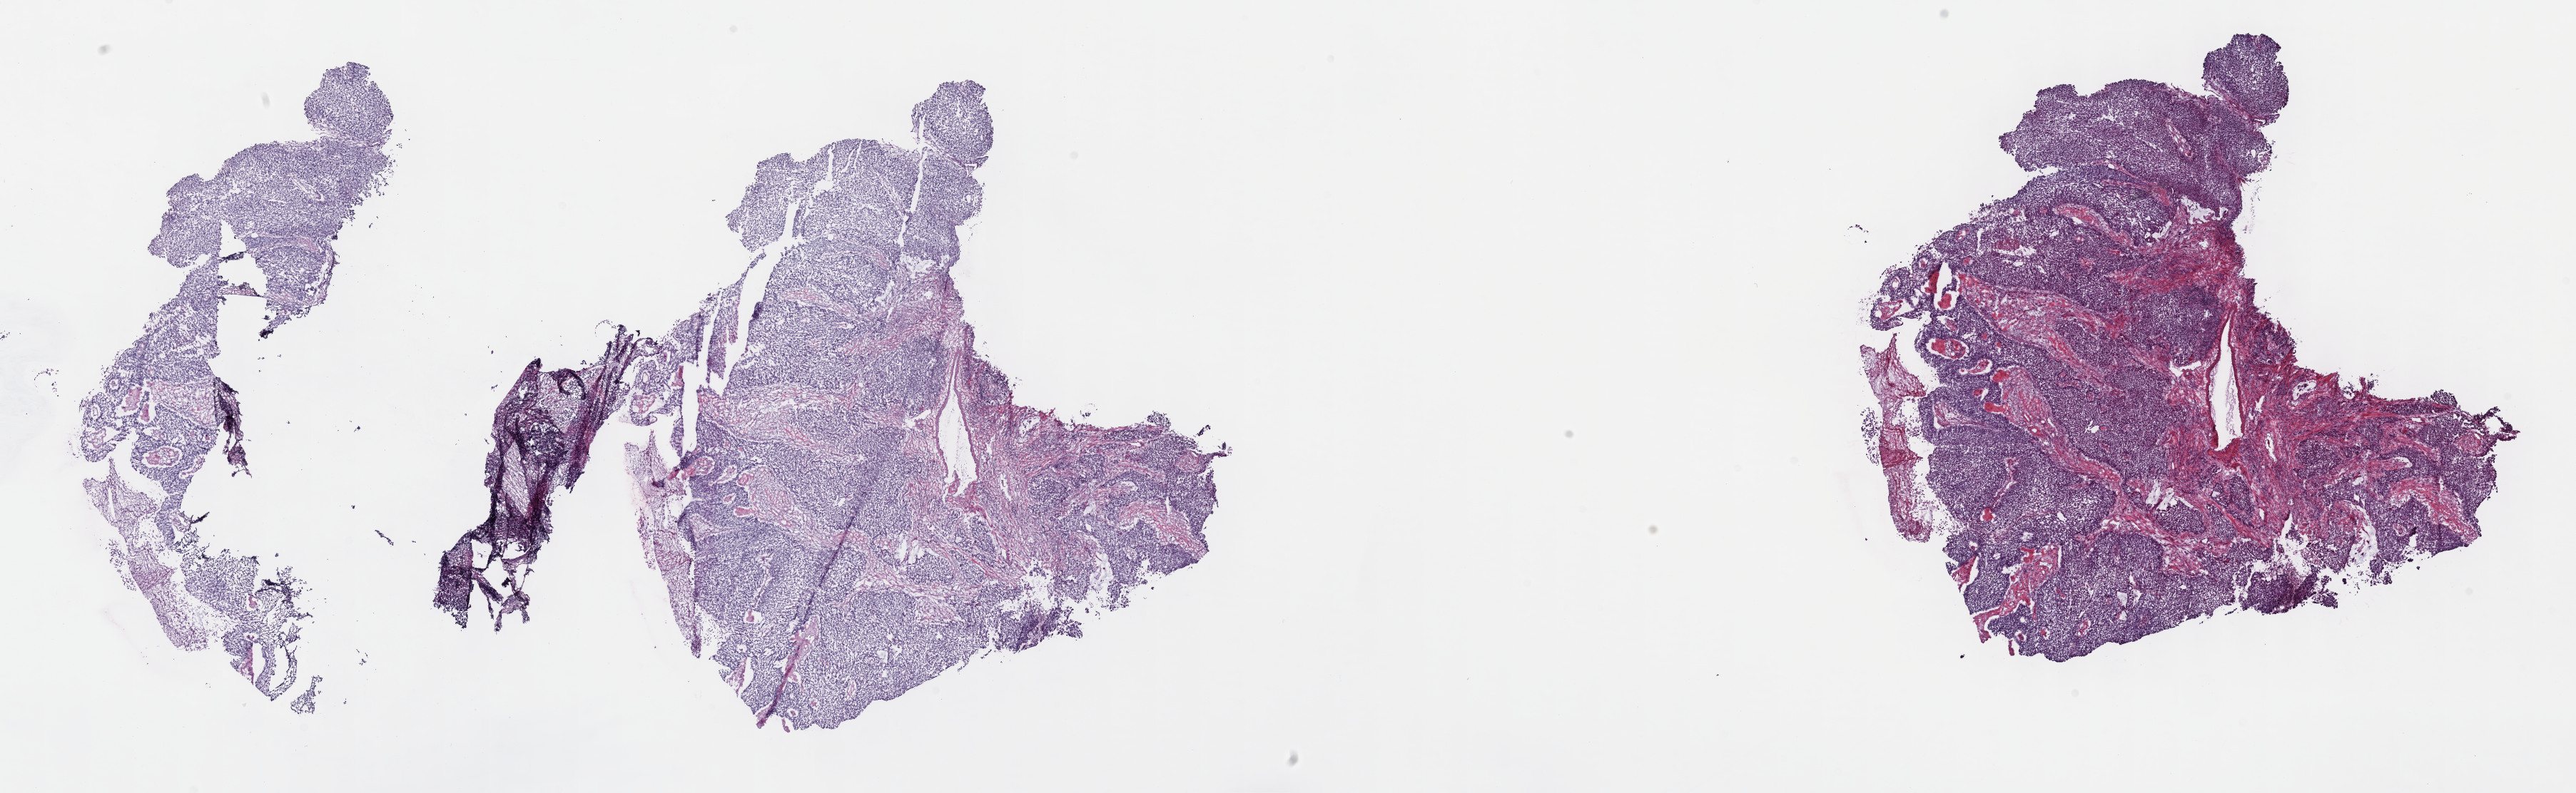
H&E-stained whole-slide image — a low-resolution overview of the entire scanned area, about 29.2 x 9.0 mm; frozen section from the top of the tissue portion; bladder, primary tumour sample. Male patient; age at initial diagnosis 71 years. Histologic grade: high grade. Composition of this section per pathologist review: tumour cells 75%, tumour nuclei 75%, normal cells 0%, stromal cells 25%, necrosis 0%. Inflammatory infiltration, as recorded: lymphocyte infiltration 3%, monocyte infiltration 1%, neutrophil infiltration 5%.
- pathologic diagnosis: Transitional cell carcinoma (lateral wall of bladder)
- AJCC pathologic stage: II (7th edition)